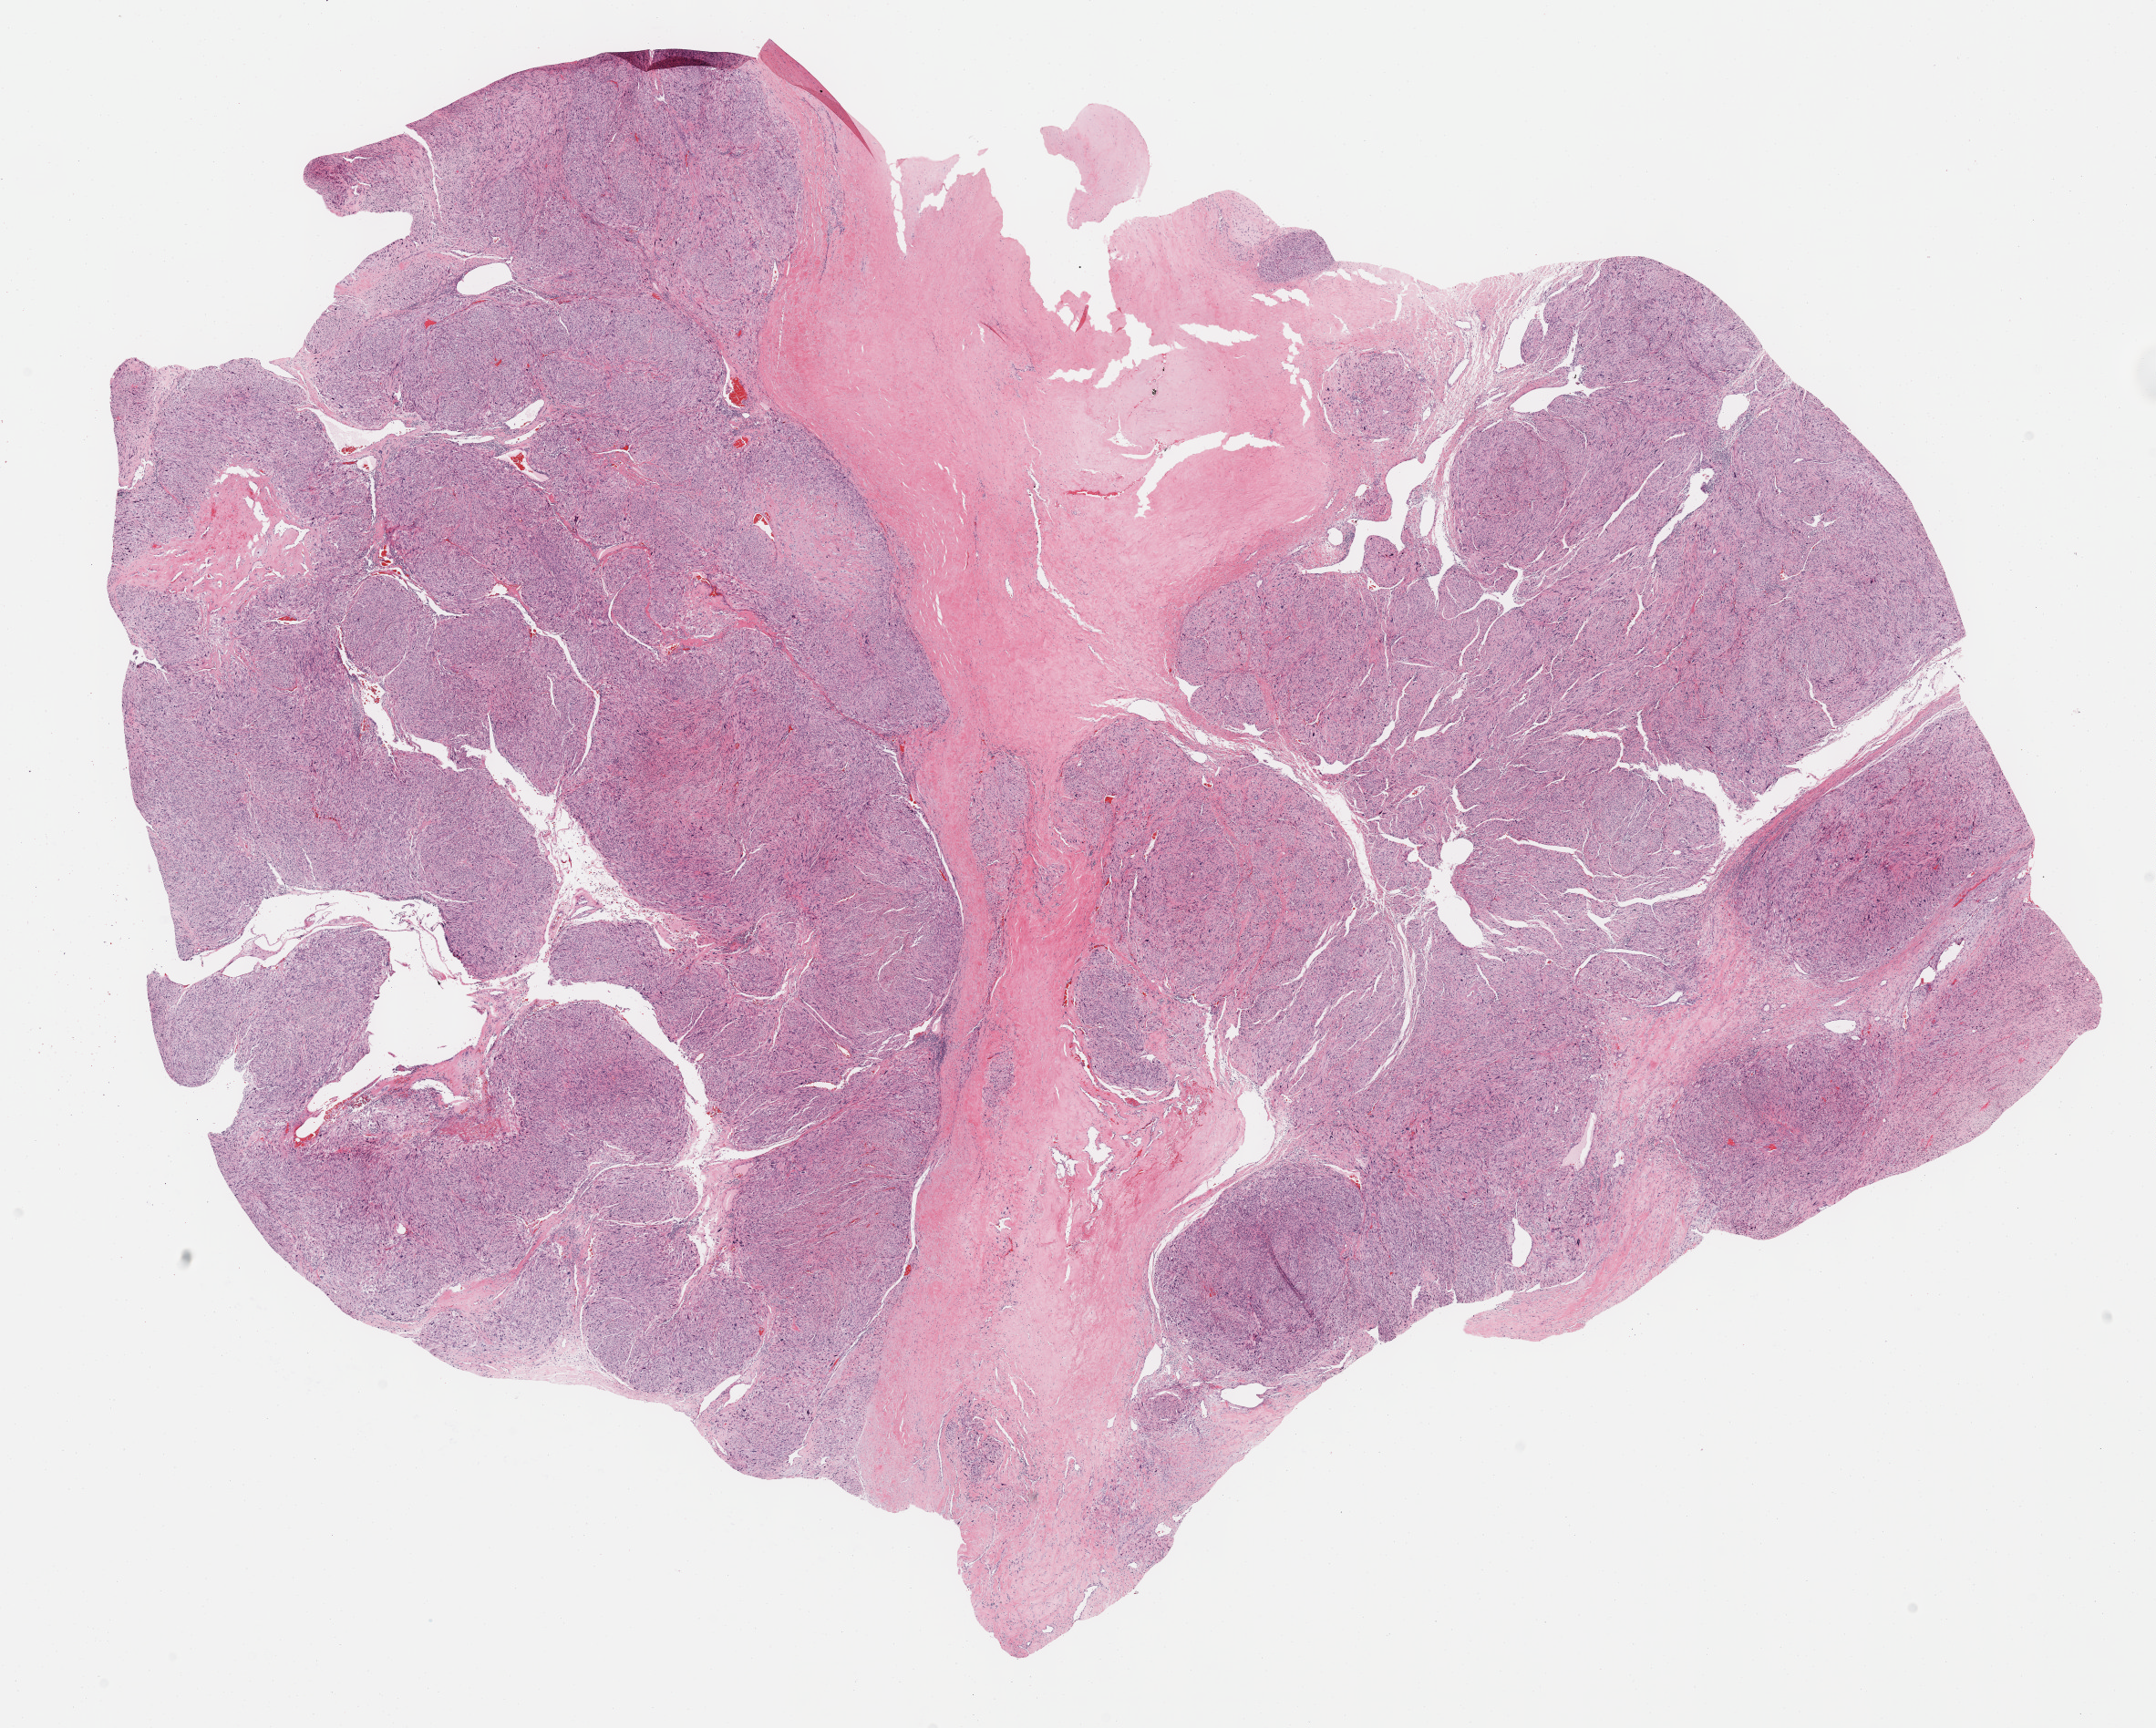
Whole-slide histology image, H&E — low-resolution overview of the scanned area, about 19.1 x 15.3 mm (slide scanned at 40x); formalin-fixed paraffin-embedded (FFPE) diagnostic section; sample: primary tumour, retroperitoneum and peritoneum. Patient sex: female.
- diagnosis: Leiomyosarcoma, NOS (retroperitoneum)